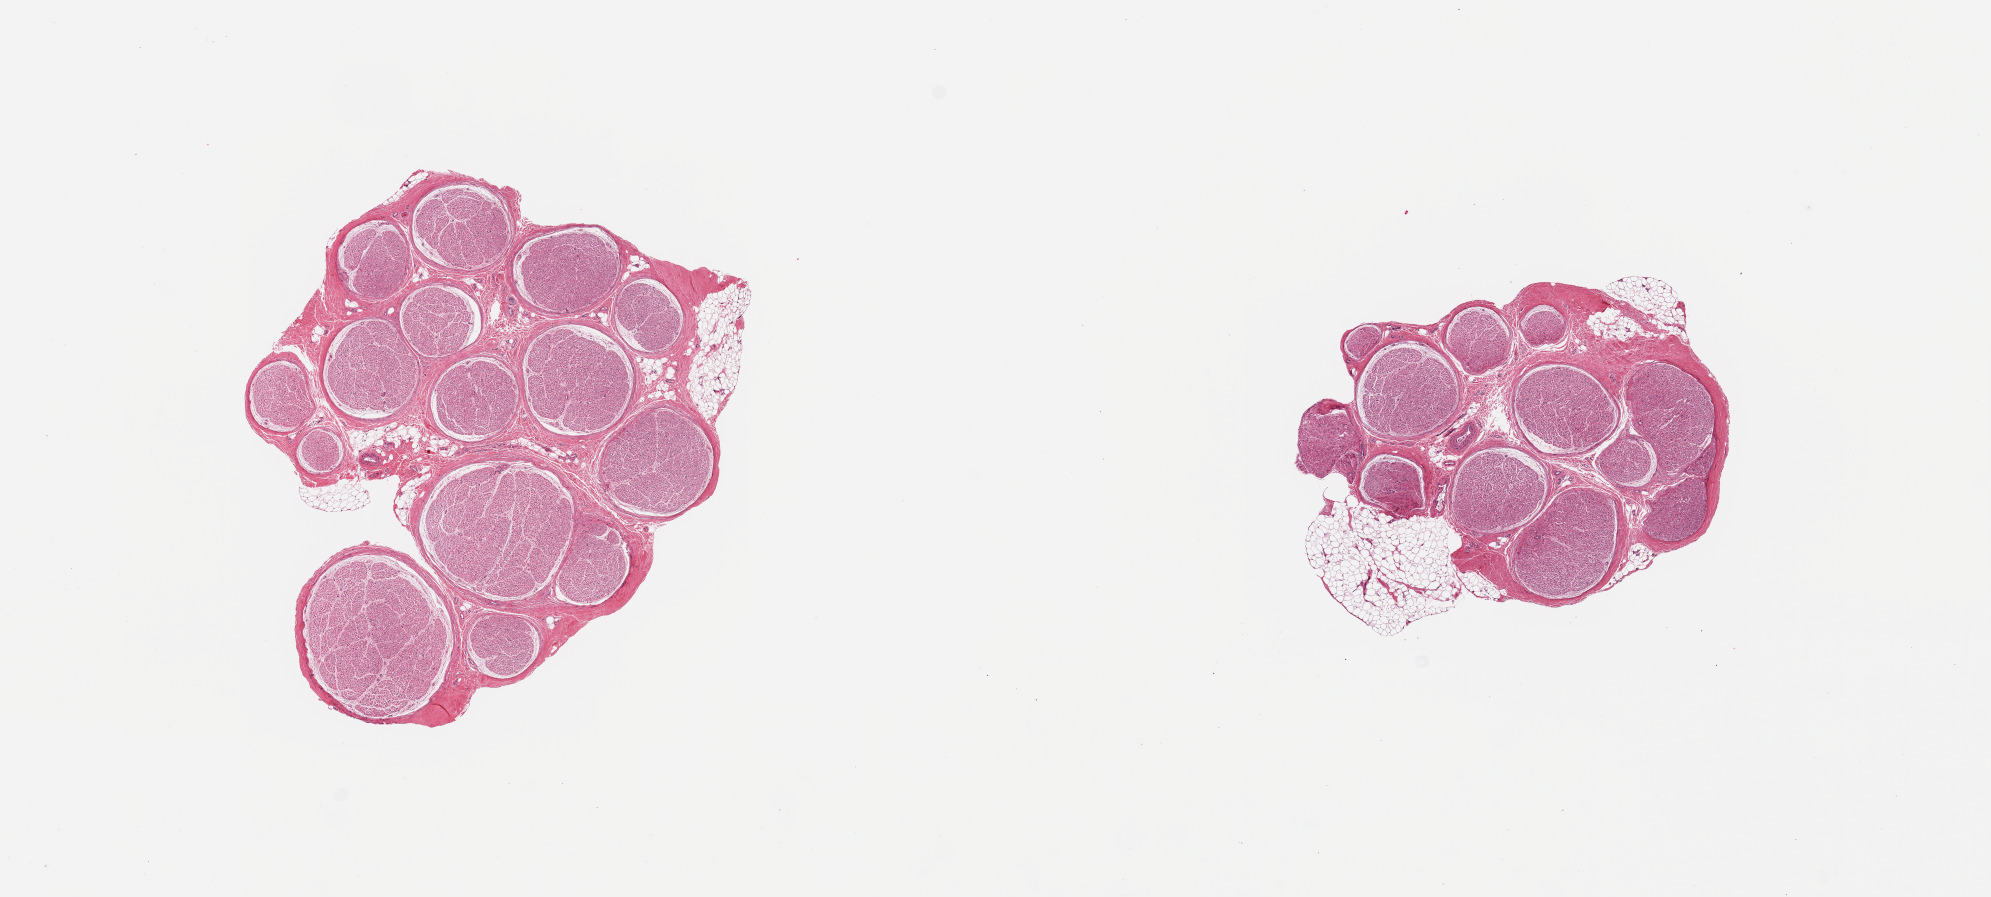
Digitized H&E-stained section, brightfield — shown as a low-resolution overview of the whole scanned area (about 15.8 x 7.1 mm, from a 20x scan); PAXgene-fixed paraffin-embedded (PFPE) section; sampled site (target tissue): tibial nerve; donor tissue sample. Female donor.
Review note (as recorded): 2 pieces, focal adherent fat but generally clean specimens.